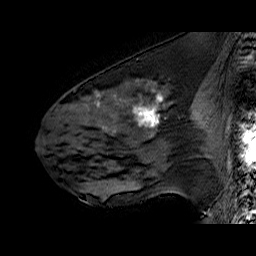
Breast MRI (dynamic contrast-enhanced), one sagittal slice. Position 28 of 60 along the scan axis. Dynamic contrast-enhanced series, time point 2 of 6 at this slice position (early post-contrast). 1.5 T. TE 6.4 ms, TR 32.9 ms. 256 × 256 image matrix, field of view 200 × 200 mm. Female patient. Case-level facts recorded for this patient, not image findings: setting: breast cancer imaged before/during neoadjuvant chemotherapy; receptor status: HER2-positive.
Annotated regions visible in this slice (semi-automatic segmentation, software-assisted and operator-edited):
- analysis volume of interest (the breast-tissue region the enhancement analysis was run in; not a lesion): bounding box <51,78,196,160> (left, top, right, bottom; pixels)
- tumour enhancement mask (voxels above the 100 % enhancement threshold inside the analysis volume of interest): <95,91,164,129>